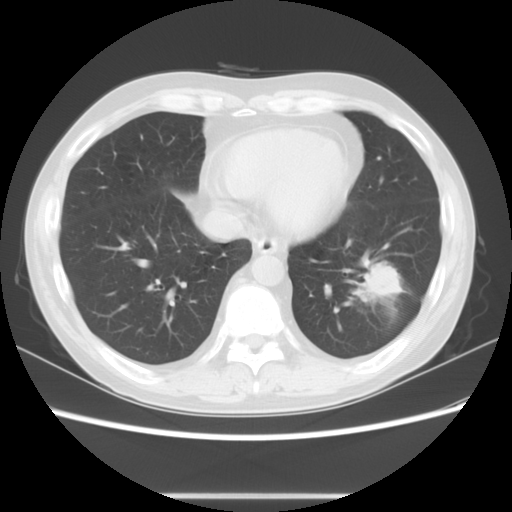
Chest CT, one axial slice; position 25 of 63 along the scan axis; 120 kVp; lung window (W 1500 / L -600 HU); 5 mm slice thickness; 512 × 512 image matrix, field of view 347 × 347 mm. Patient: male, 49 years. From the clinical record (not read from this slice): clinical TNM (as recorded): T3 N0 M0.
Structures marked on this image (rectangle marked by the reading radiologist):
- lung tumour (recorded histology: squamous cell carcinoma): box from (x=357, y=258) to (x=414, y=306) px